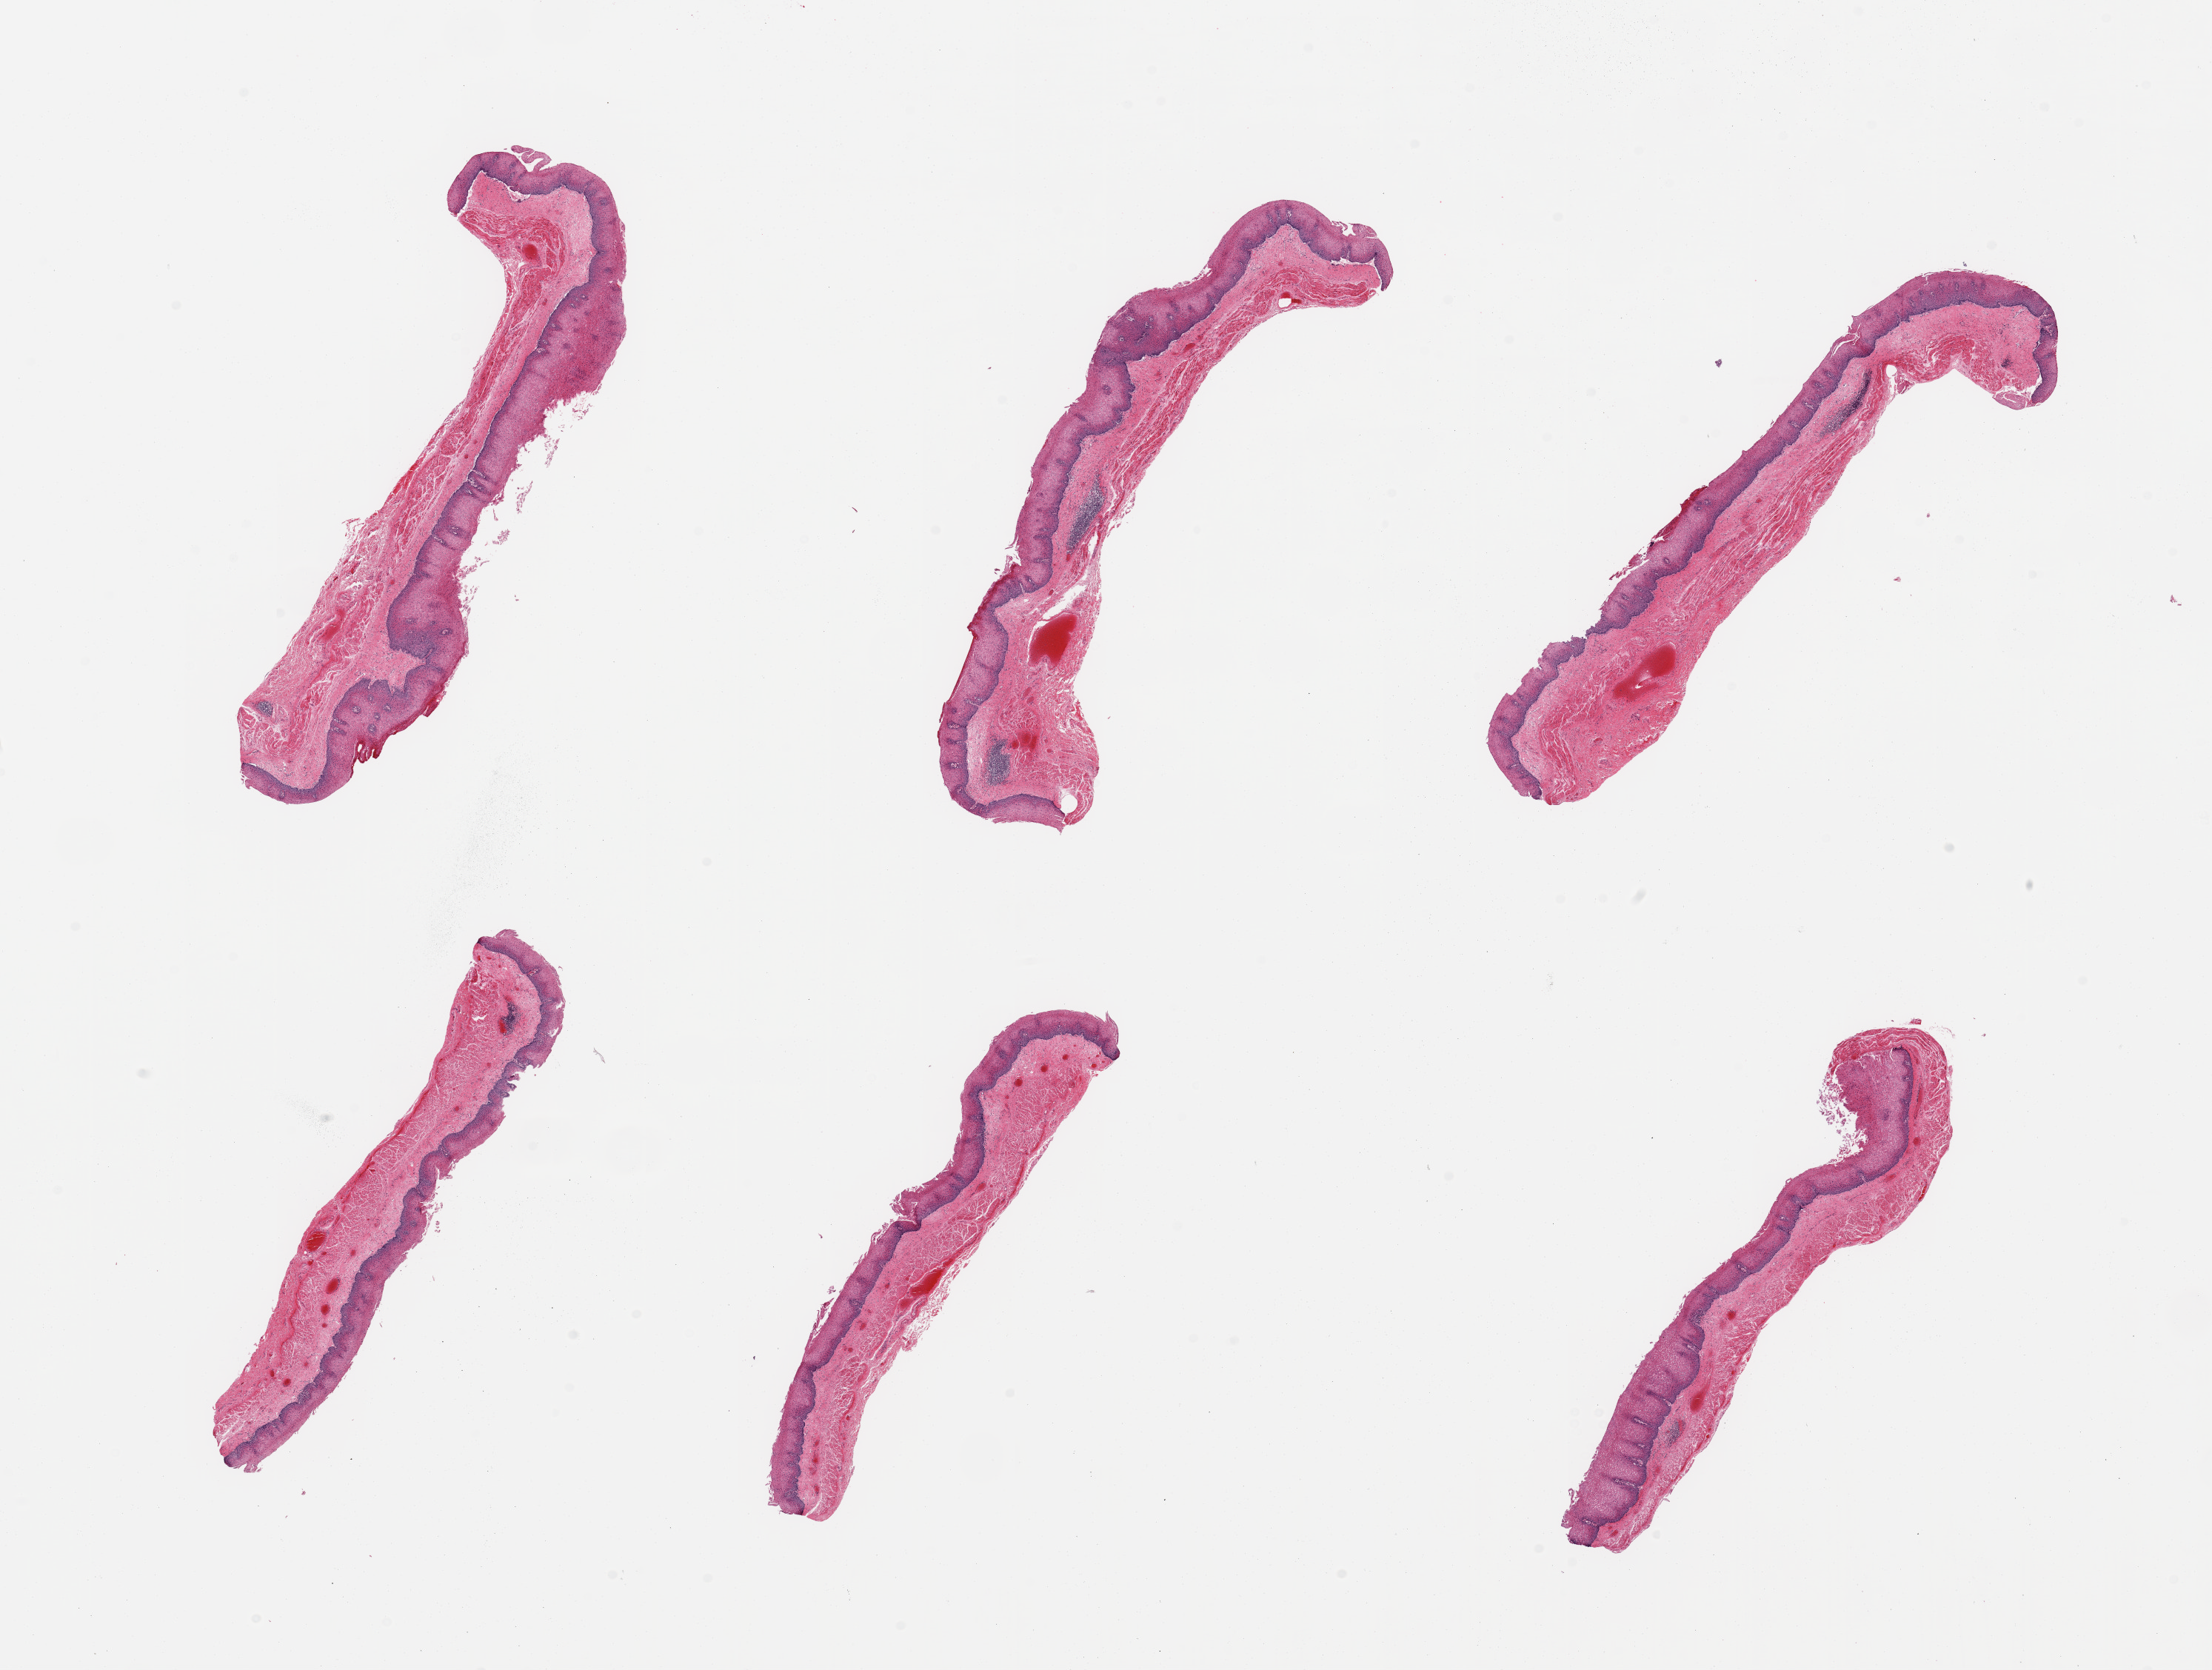
Whole-slide image, haematoxylin and eosin stain — low-resolution overview of the scanned area, about 23.6 x 17.8 mm (acquisition: 20x scan). PAXgene-fixed paraffin-embedded (PFPE) section. Section of esophageal mucous membrane (target tissue). Tissue donor sample. Donor sex: male.
Pathologist's review note for this sample: 6 pieces; congested mucosa; ~0.3mm thick squamous epithelium.